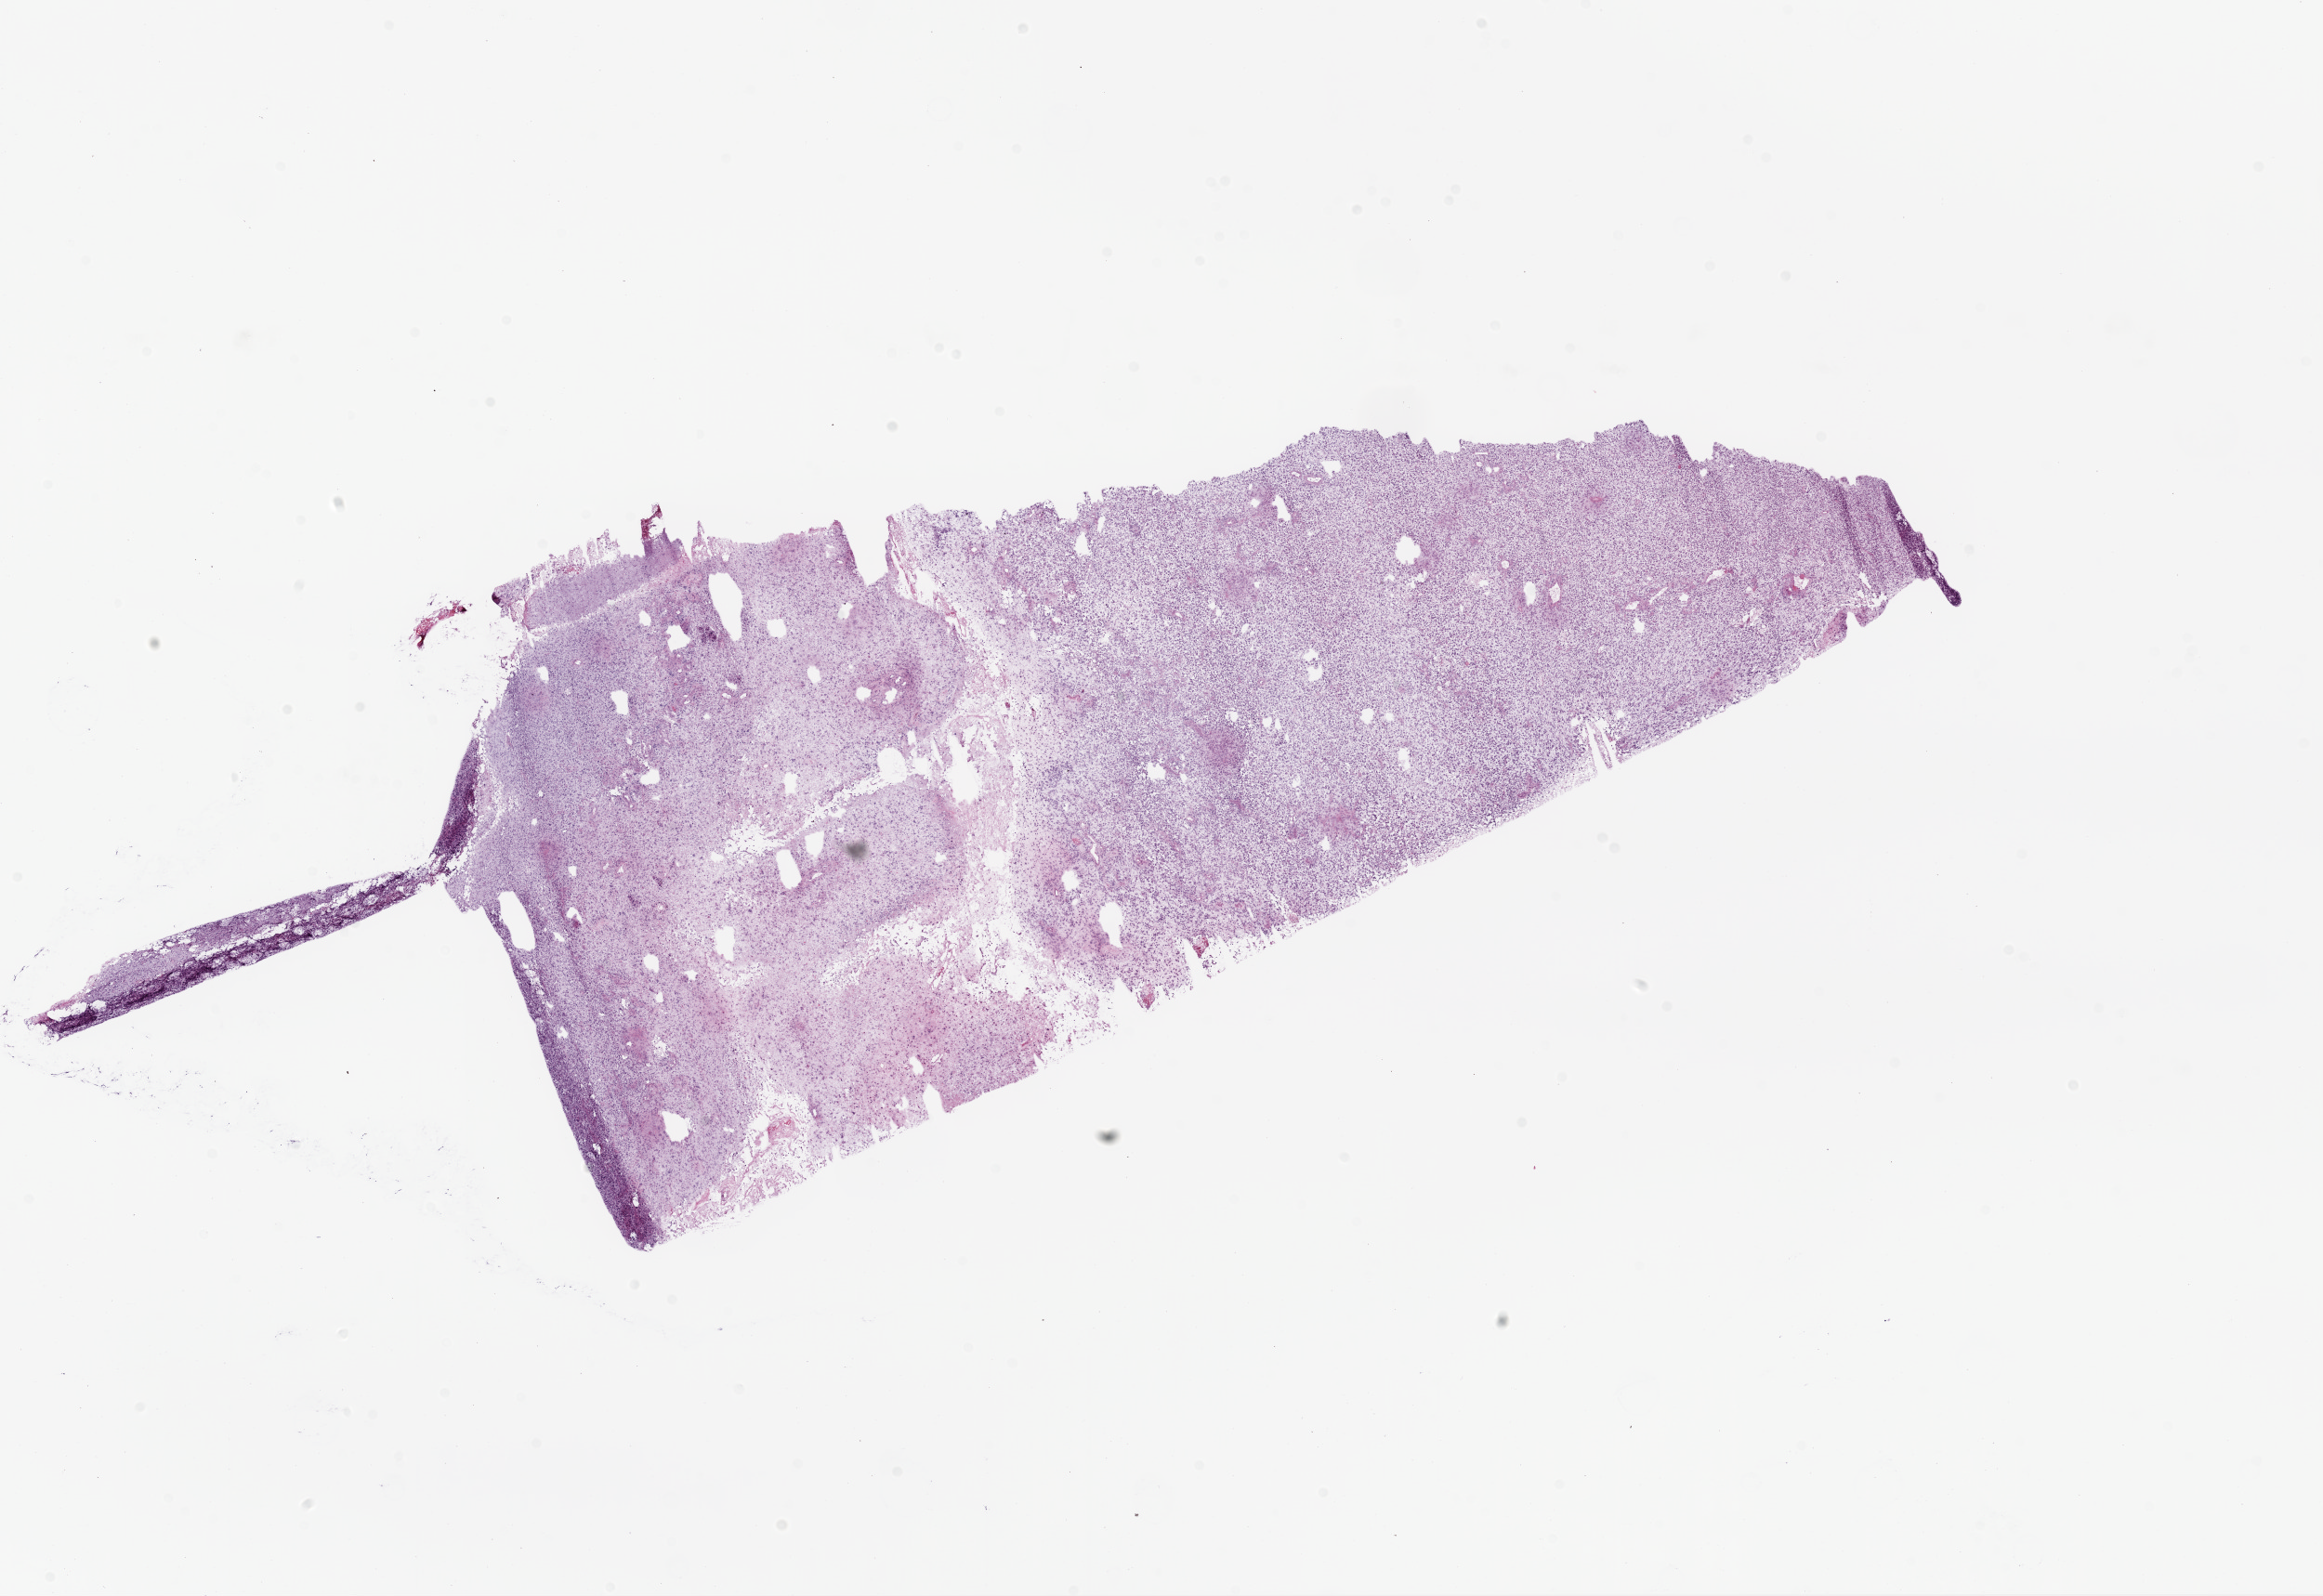
Whole-slide histology image, Hematoxylin and eosin (H&E) stained, low-resolution overview of the scanned area, about 20.1 x 13.8 mm. Frozen section. Brain, primary tumour sample. Patient: female, age at initial diagnosis 21 years. Pathologist review of this section (percent, as recorded): tumour cells 100%, tumour nuclei 85%, normal cells 0%, stromal cells 0%, necrosis 0%.
* pathologic diagnosis: Glioblastoma